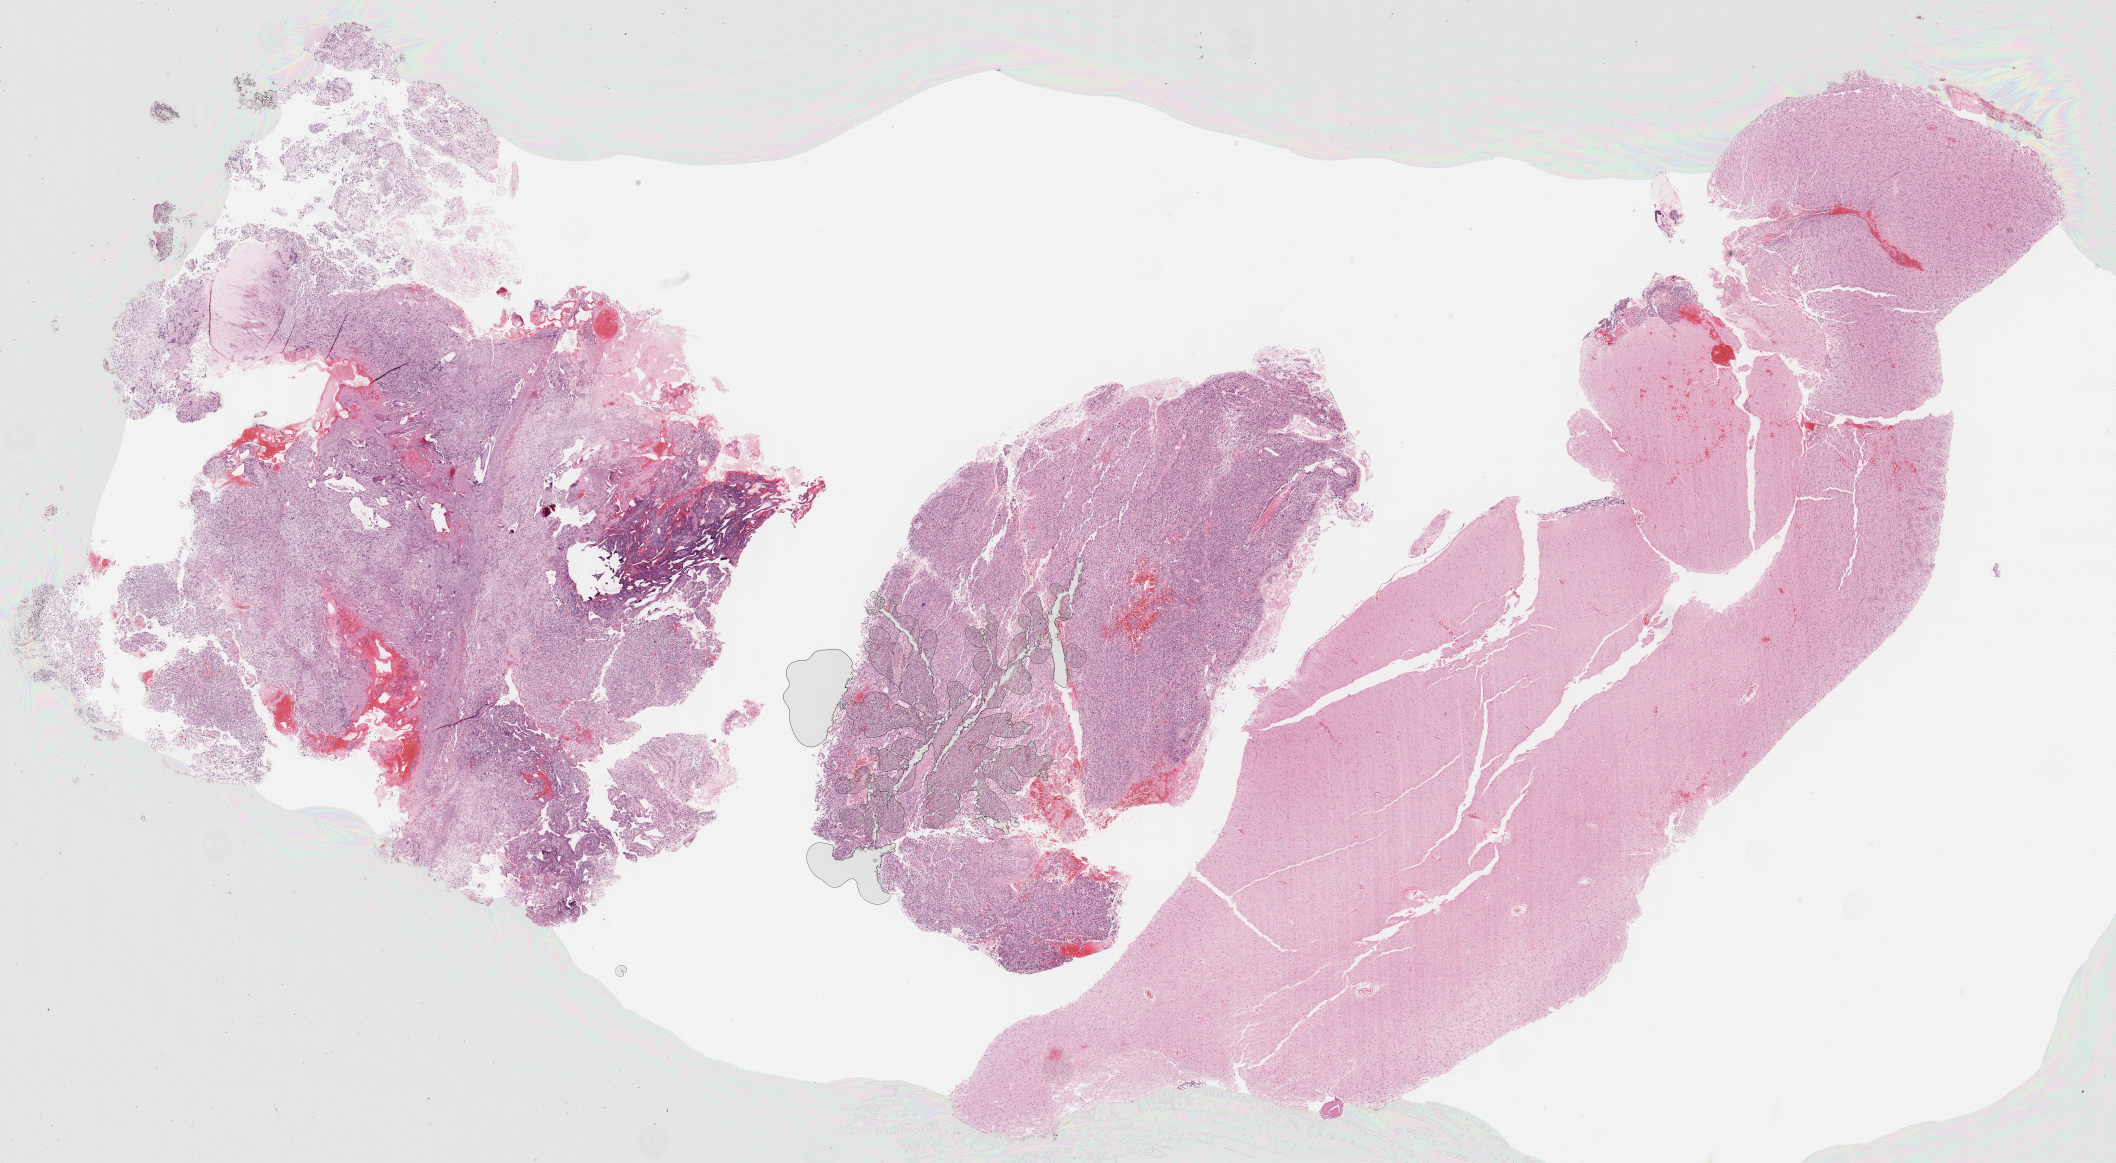
Whole-slide histology image, H&E — low-resolution overview of the scanned area, about 34.2 x 18.8 mm (acquisition: 40x scan); FFPE section; primary tumour sample from the brain. Male, age 58 years at initial diagnosis.
- histologic diagnosis: Glioblastoma